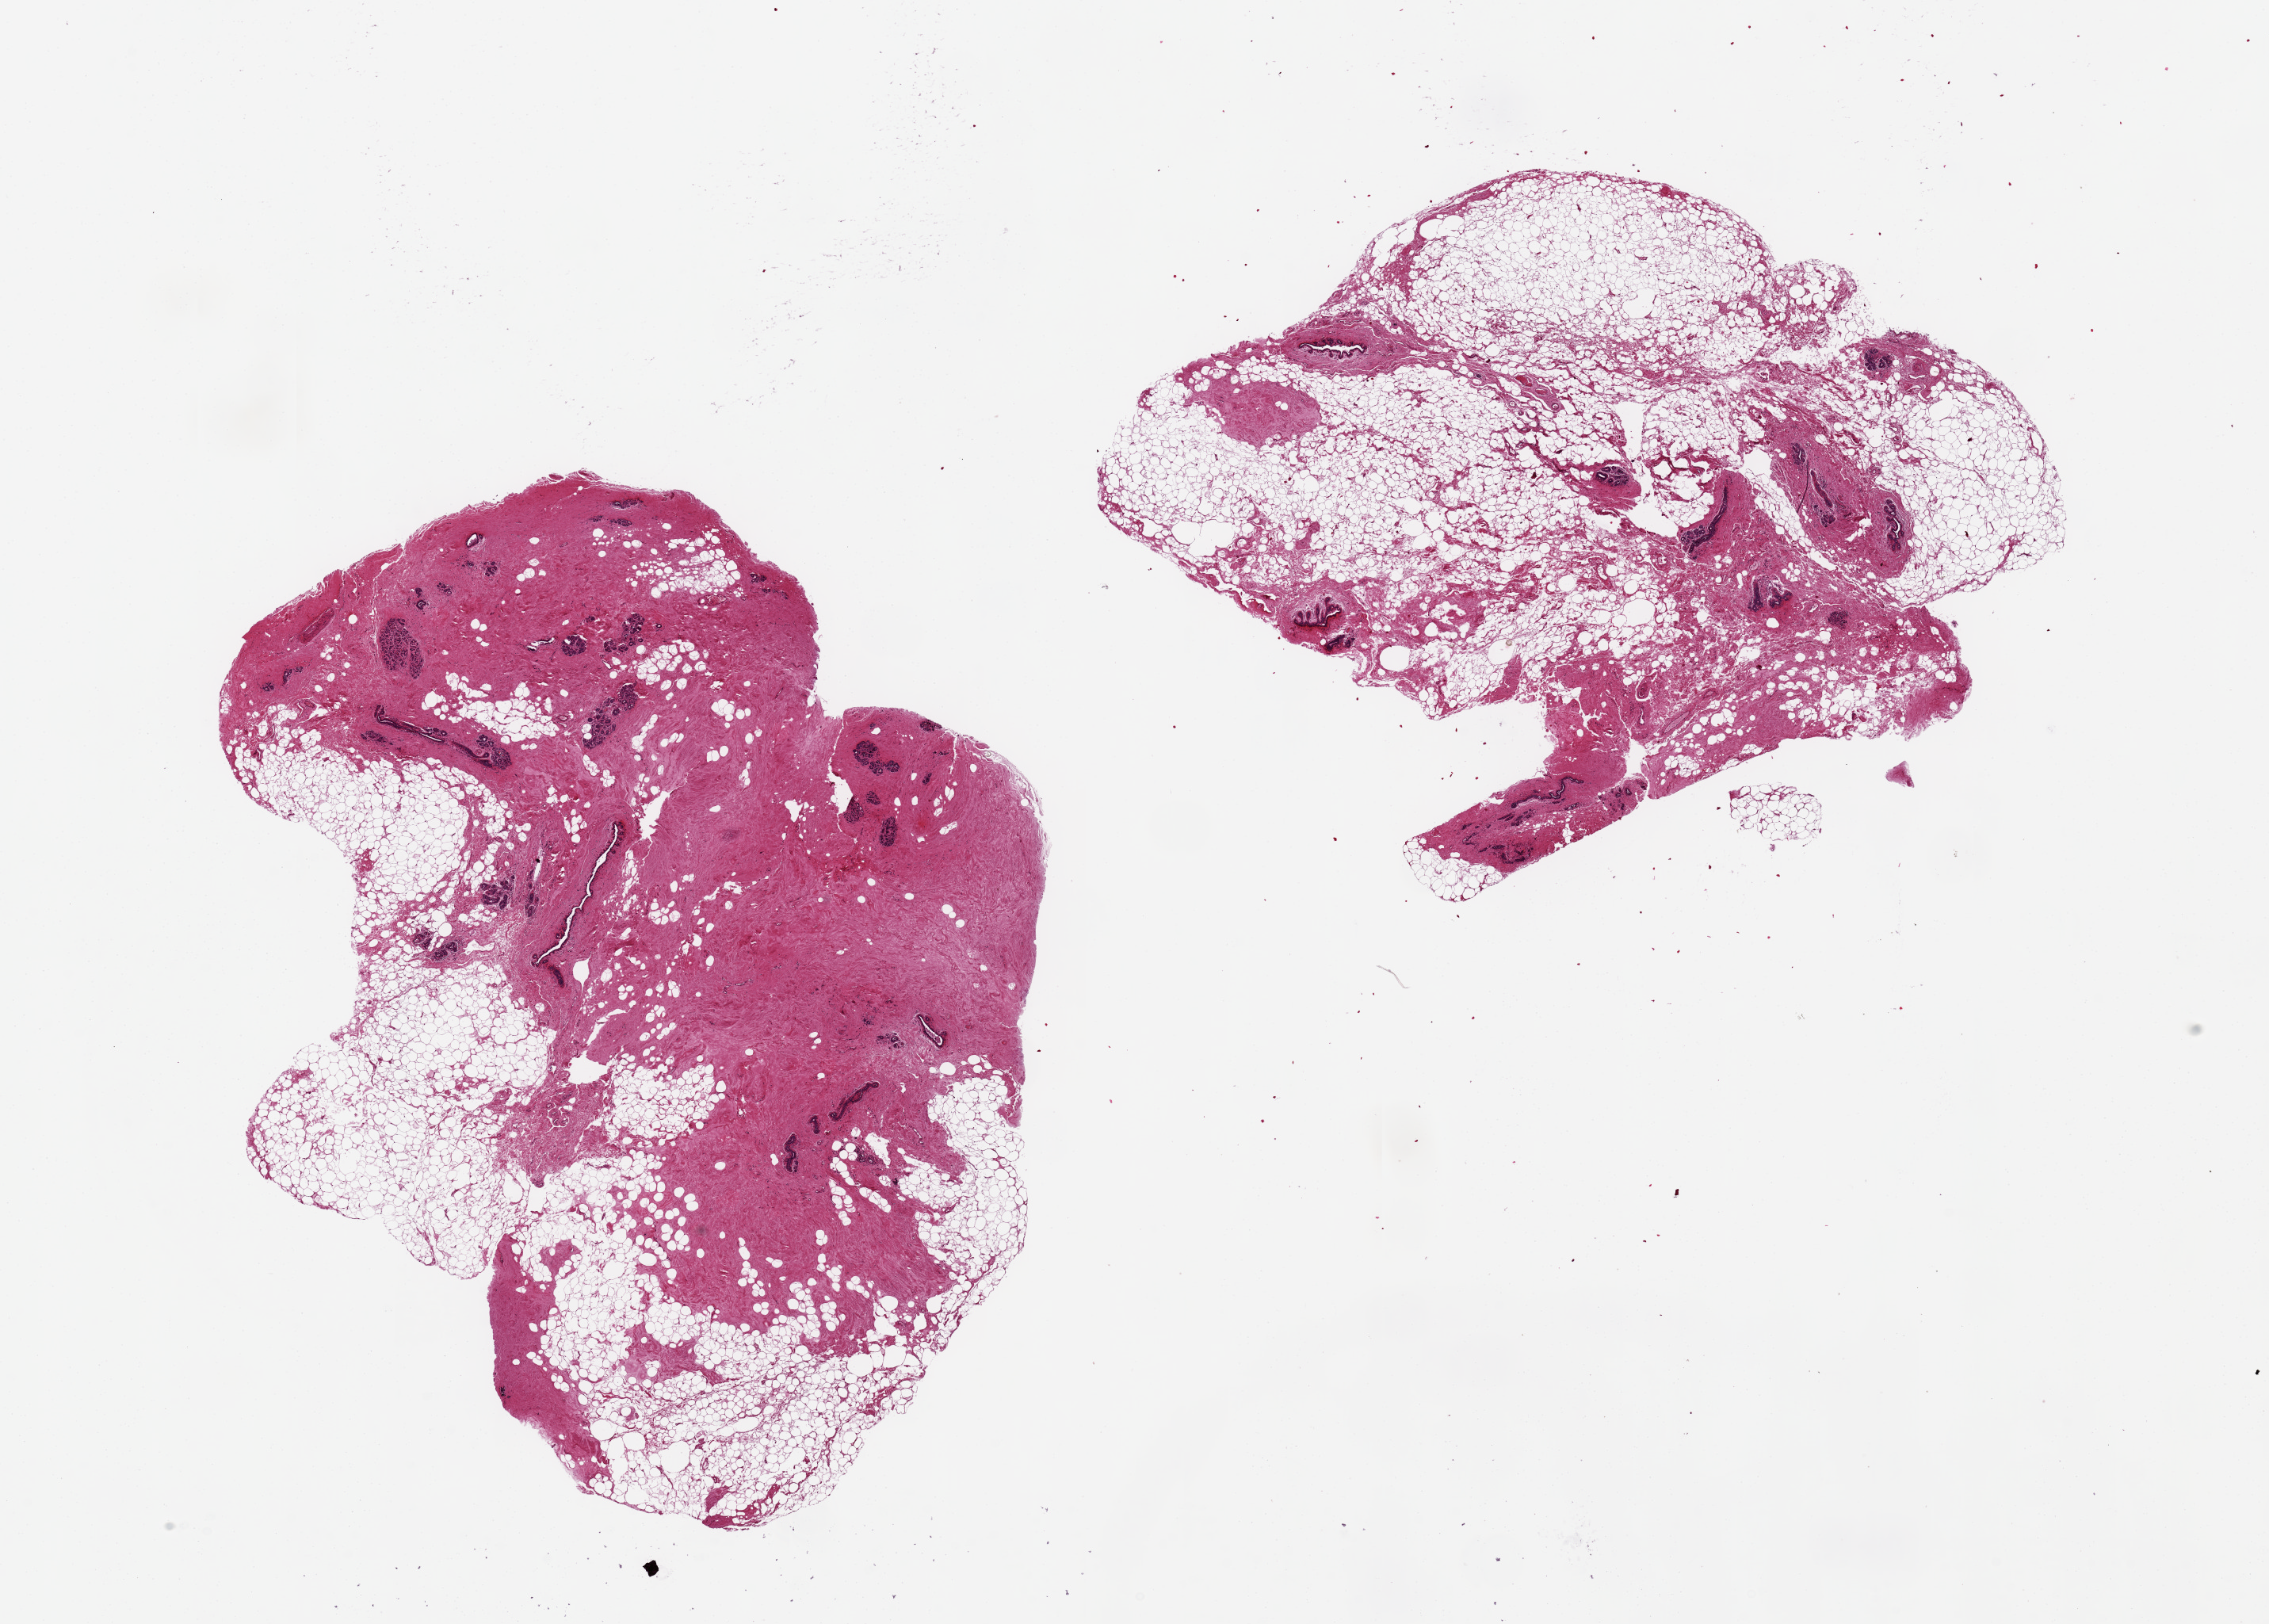
Digitized haematoxylin and eosin-stained section, whole scanned area (about 22.6 x 16.2 mm) shown as a low-resolution overview; PAXgene-fixed paraffin-embedded (PFPE) section; section of breast (target tissue); donor tissue sample. Donor sex: female.
Reviewer comment on this tissue sample: 2 aliquots, ~9x7mm. Multiple atrophic TDLUs noted on images.